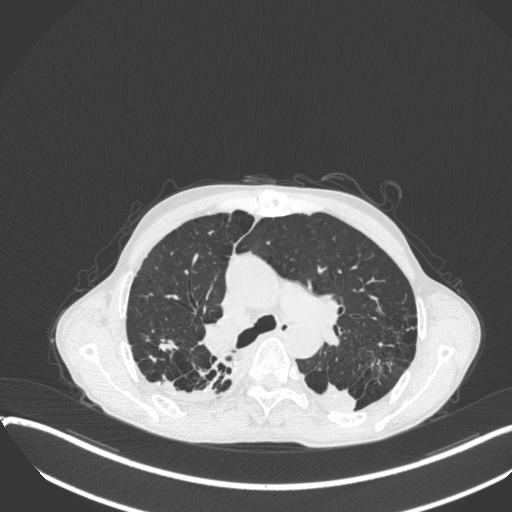
Chest CT, one axial slice; 120 kVp; lung window (W 1500 / L -600 HU); 1 mm slice thickness; 512 × 512 image matrix, field of view 400 × 400 mm. Patient: male, 57 years. Case-level facts recorded for this patient, not image findings: clinical TNM (as recorded): T4 N0 M0.
Outlined on this slice (bounding box drawn by a radiologist):
- lung tumour (recorded histology: squamous cell carcinoma): box from (x=308, y=378) to (x=359, y=417) px